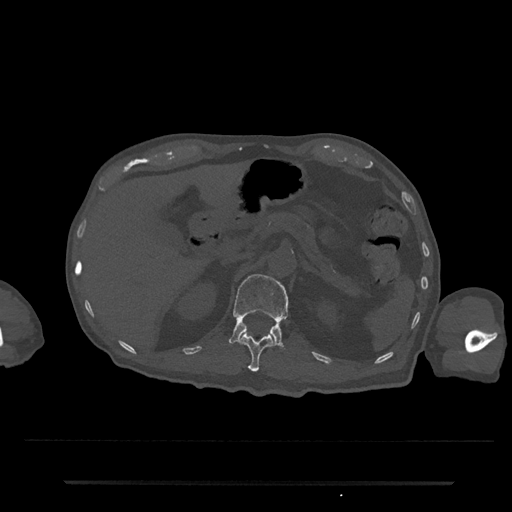
CT including the spine, one axial slice. Position 161 of 797 along the scan axis. Reconstruction kernel Br40s/3. 120 kVp. Bone window (W 1800 / L 400 HU). 0.5 mm slice thickness. 512 × 512 image matrix, field of view 427 × 427 mm. Male patient, age 74 years. From the clinical record (not read from this slice): primary cancer: prostate.
Structures marked on this image (semi-automatically segmented with operator editing):
- L1 vertebra: box from (x=229, y=274) to (x=289, y=346) px
- T12 vertebra: (x=240, y=333)–(x=273, y=372)